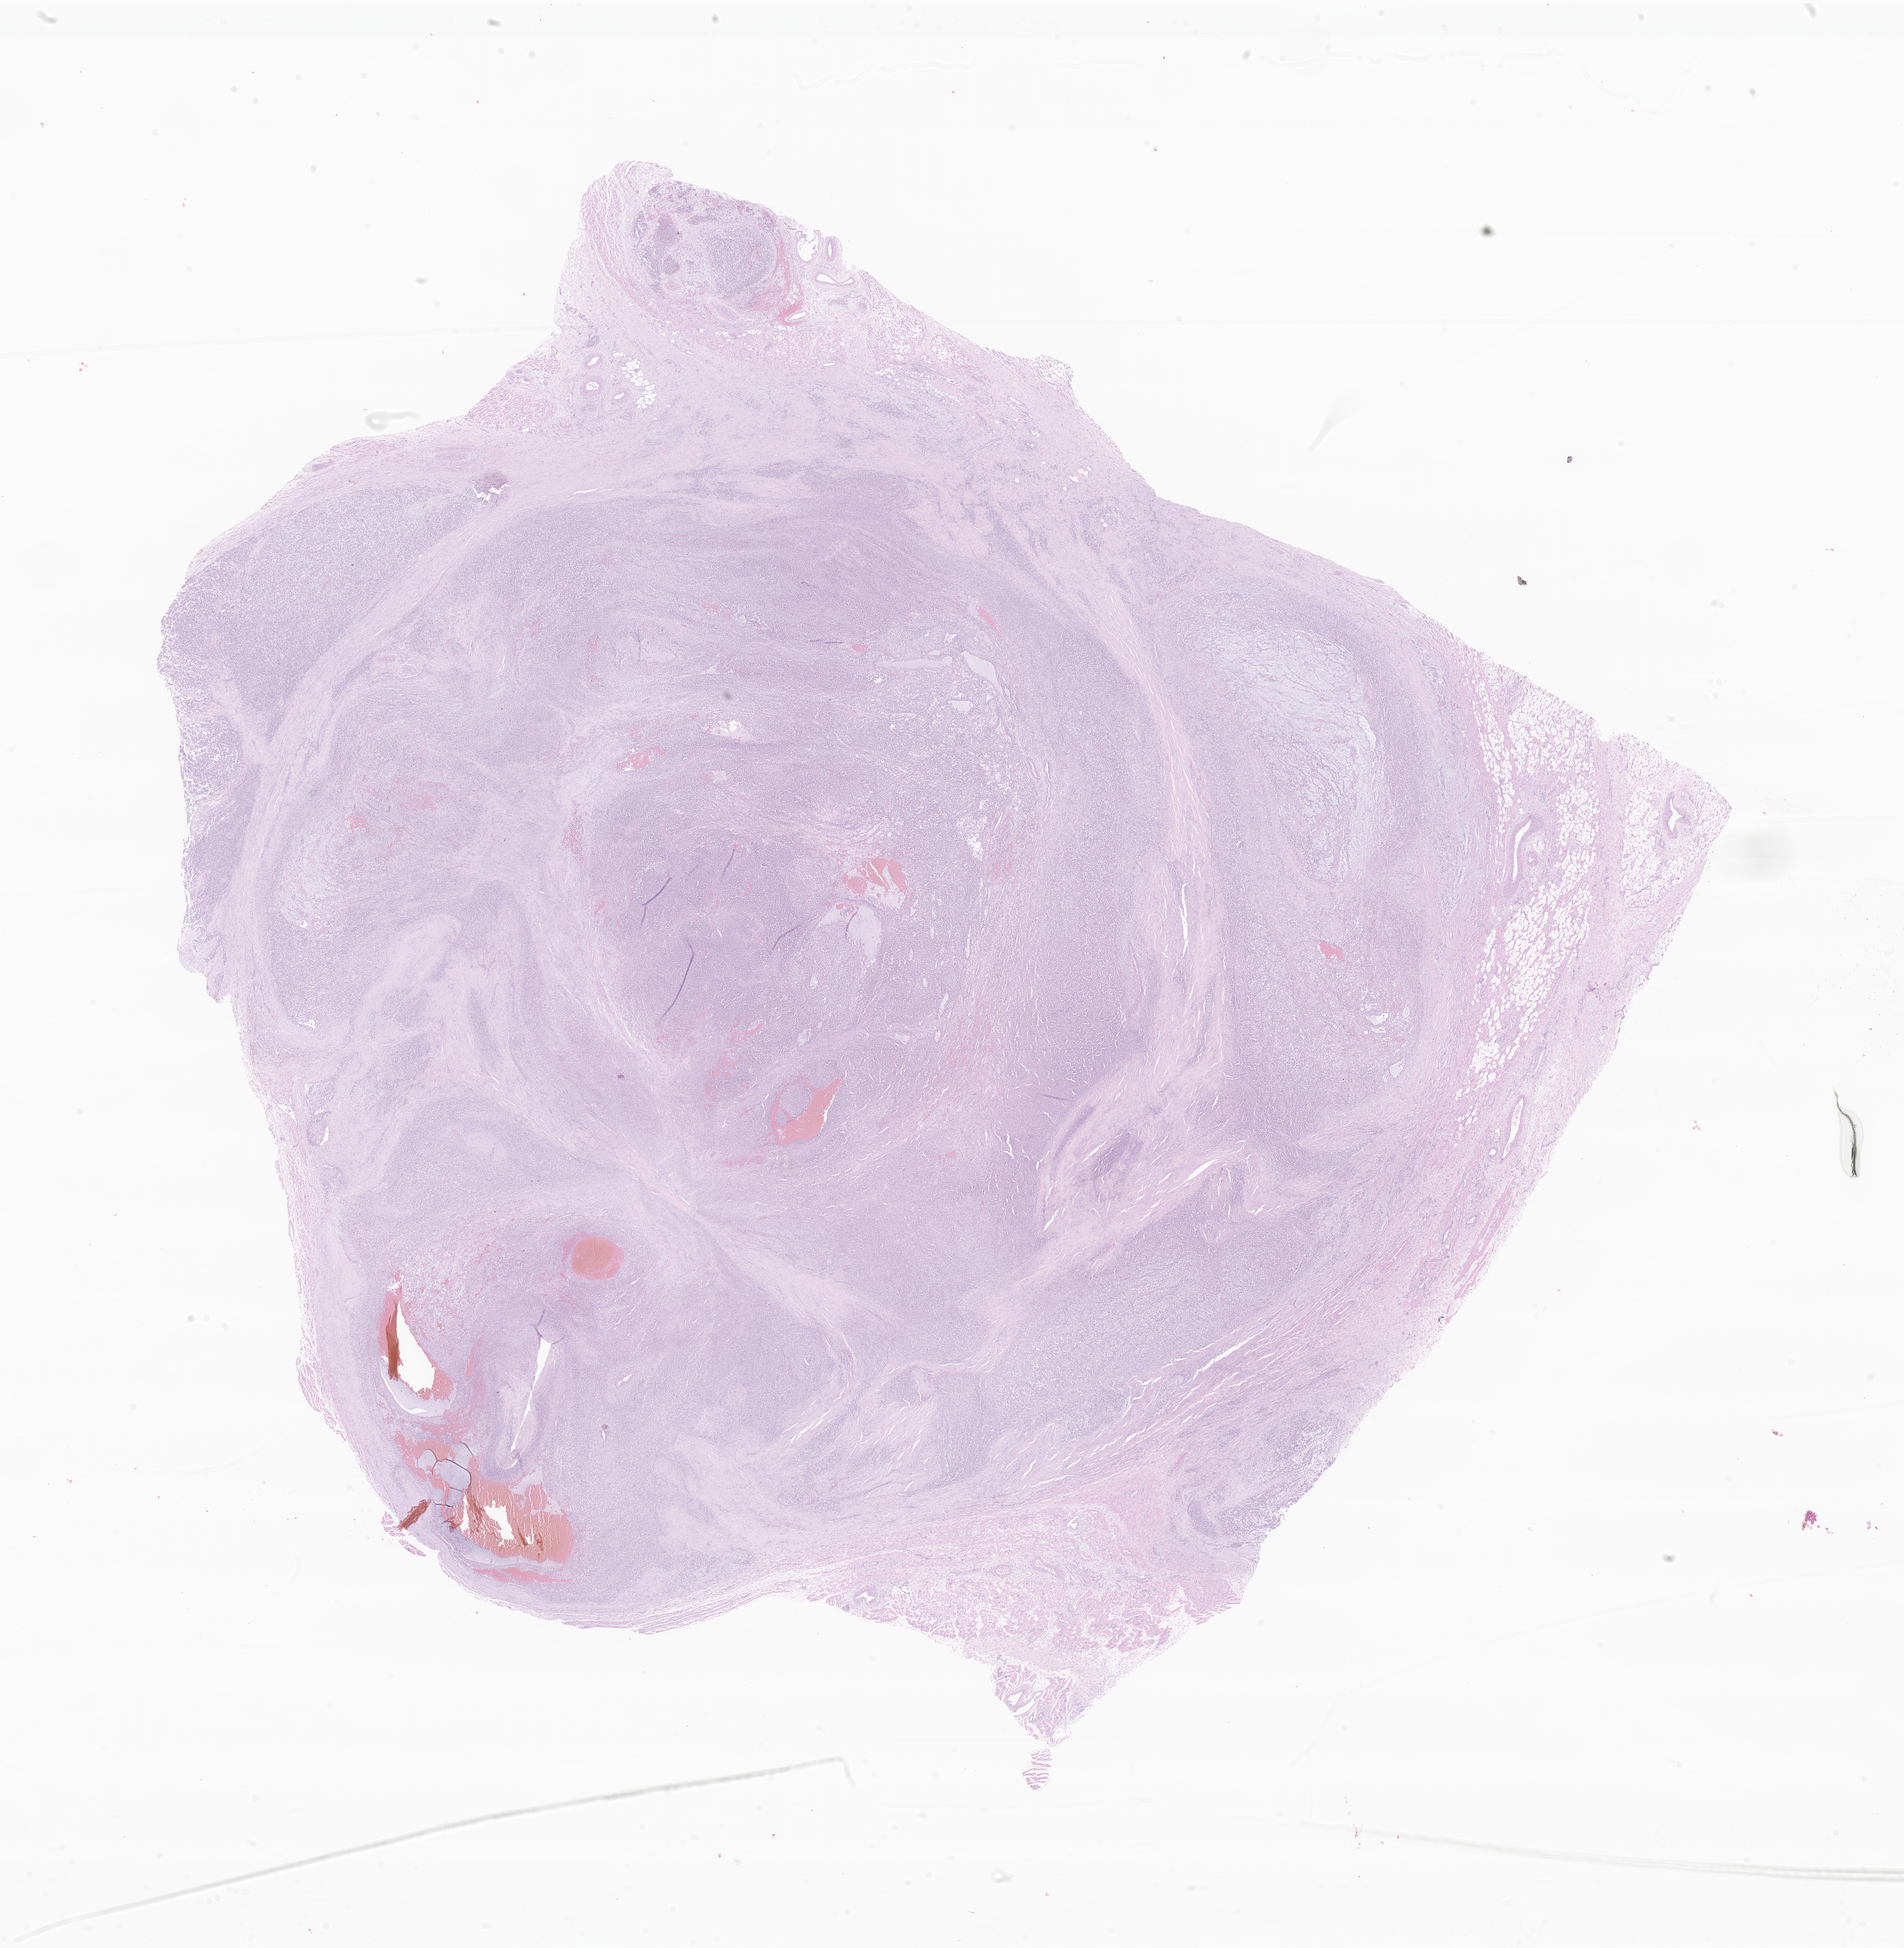
Whole-slide image, hematoxylin and eosin (H&E) stain of tumor tissue from the soft tissue — a low-resolution overview of the entire scanned area, about 22.3 x 22.8 mm, formalin-fixed, paraffin-embedded (FFPE) tissue. Patient female; age 333 days.
- diagnosis: Undifferentiated sarcoma